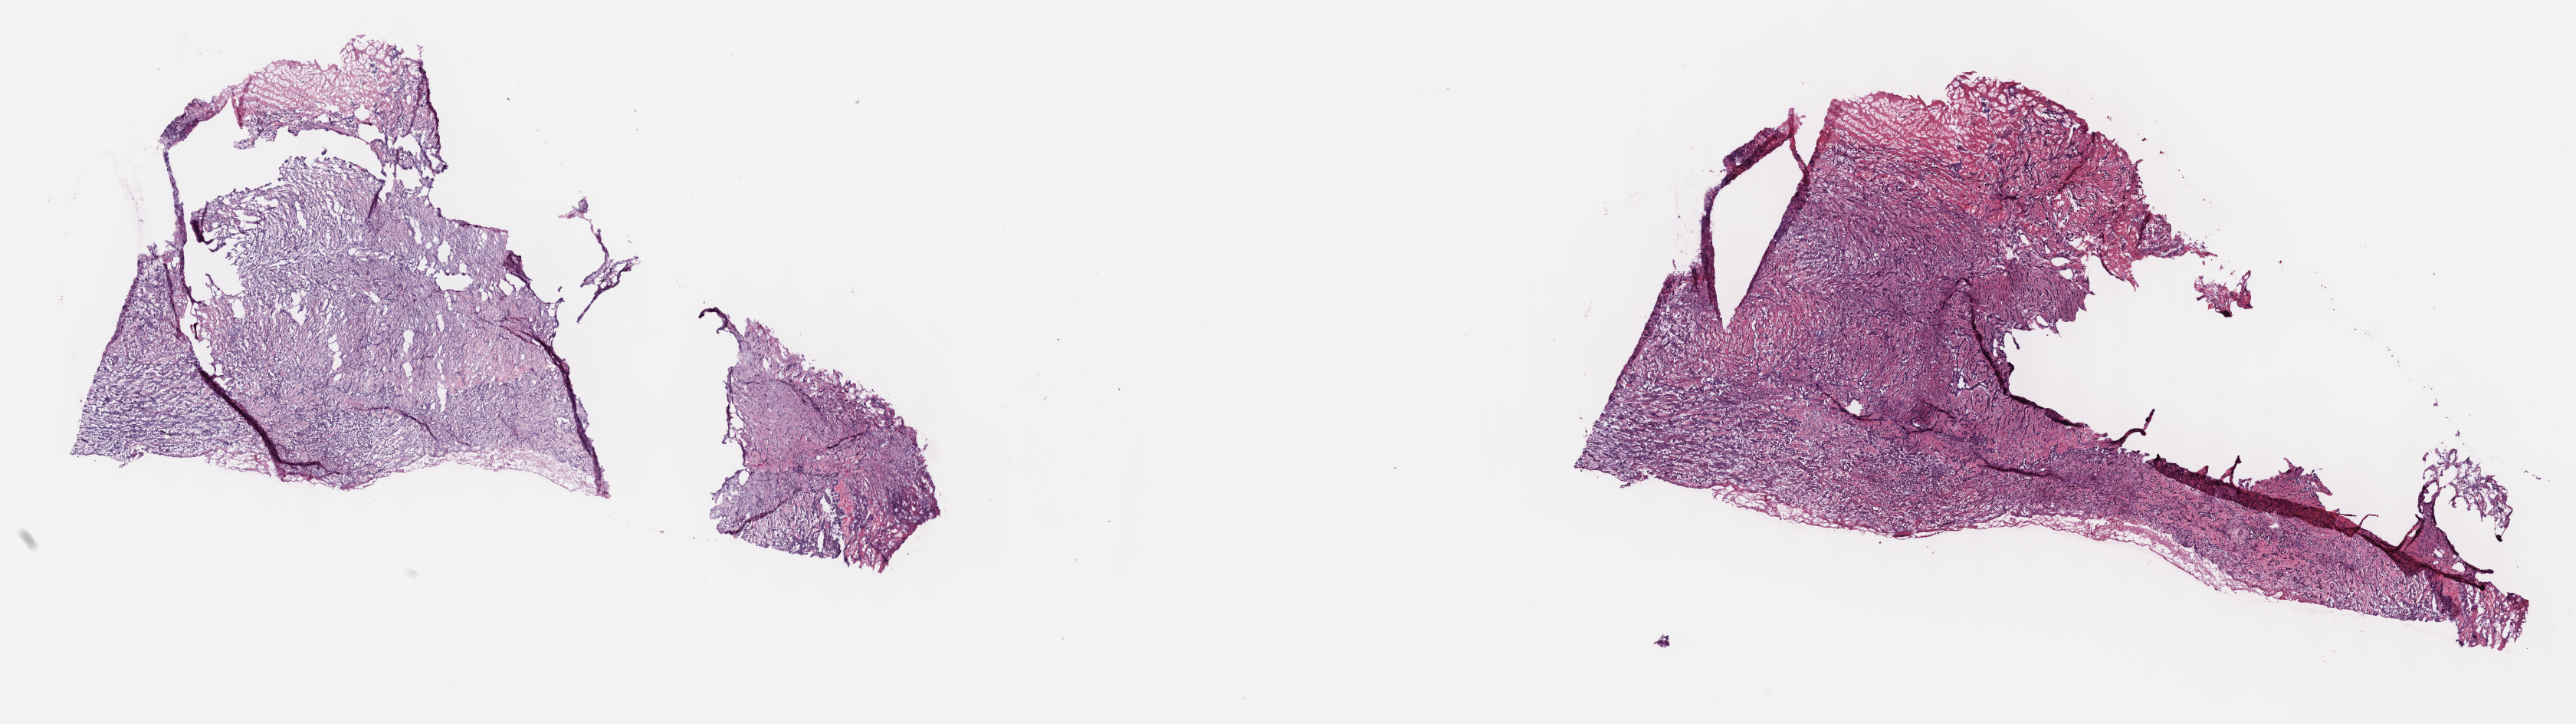
Digitized Hematoxylin and eosin (H&E) stained tissue section (whole slide) — low-resolution overview of the scanned area, about 27.2 x 7.6 mm. Frozen section. Primary tumour sample from the mesothelium. Male patient; age at initial diagnosis 66 years. Slide review estimates, as recorded: tumour cells 90%, tumour nuclei 70%, normal cells 10%, stromal cells 0%, necrosis 0%. Infiltration values recorded for this section: lymphocyte infiltration 5%, monocyte infiltration 0%, neutrophil infiltration 0%.
AJCC pathologic stage: III (7th edition). Pathologic diagnosis: Epithelioid mesothelioma, malignant (pleura, NOS). Laterality: right.